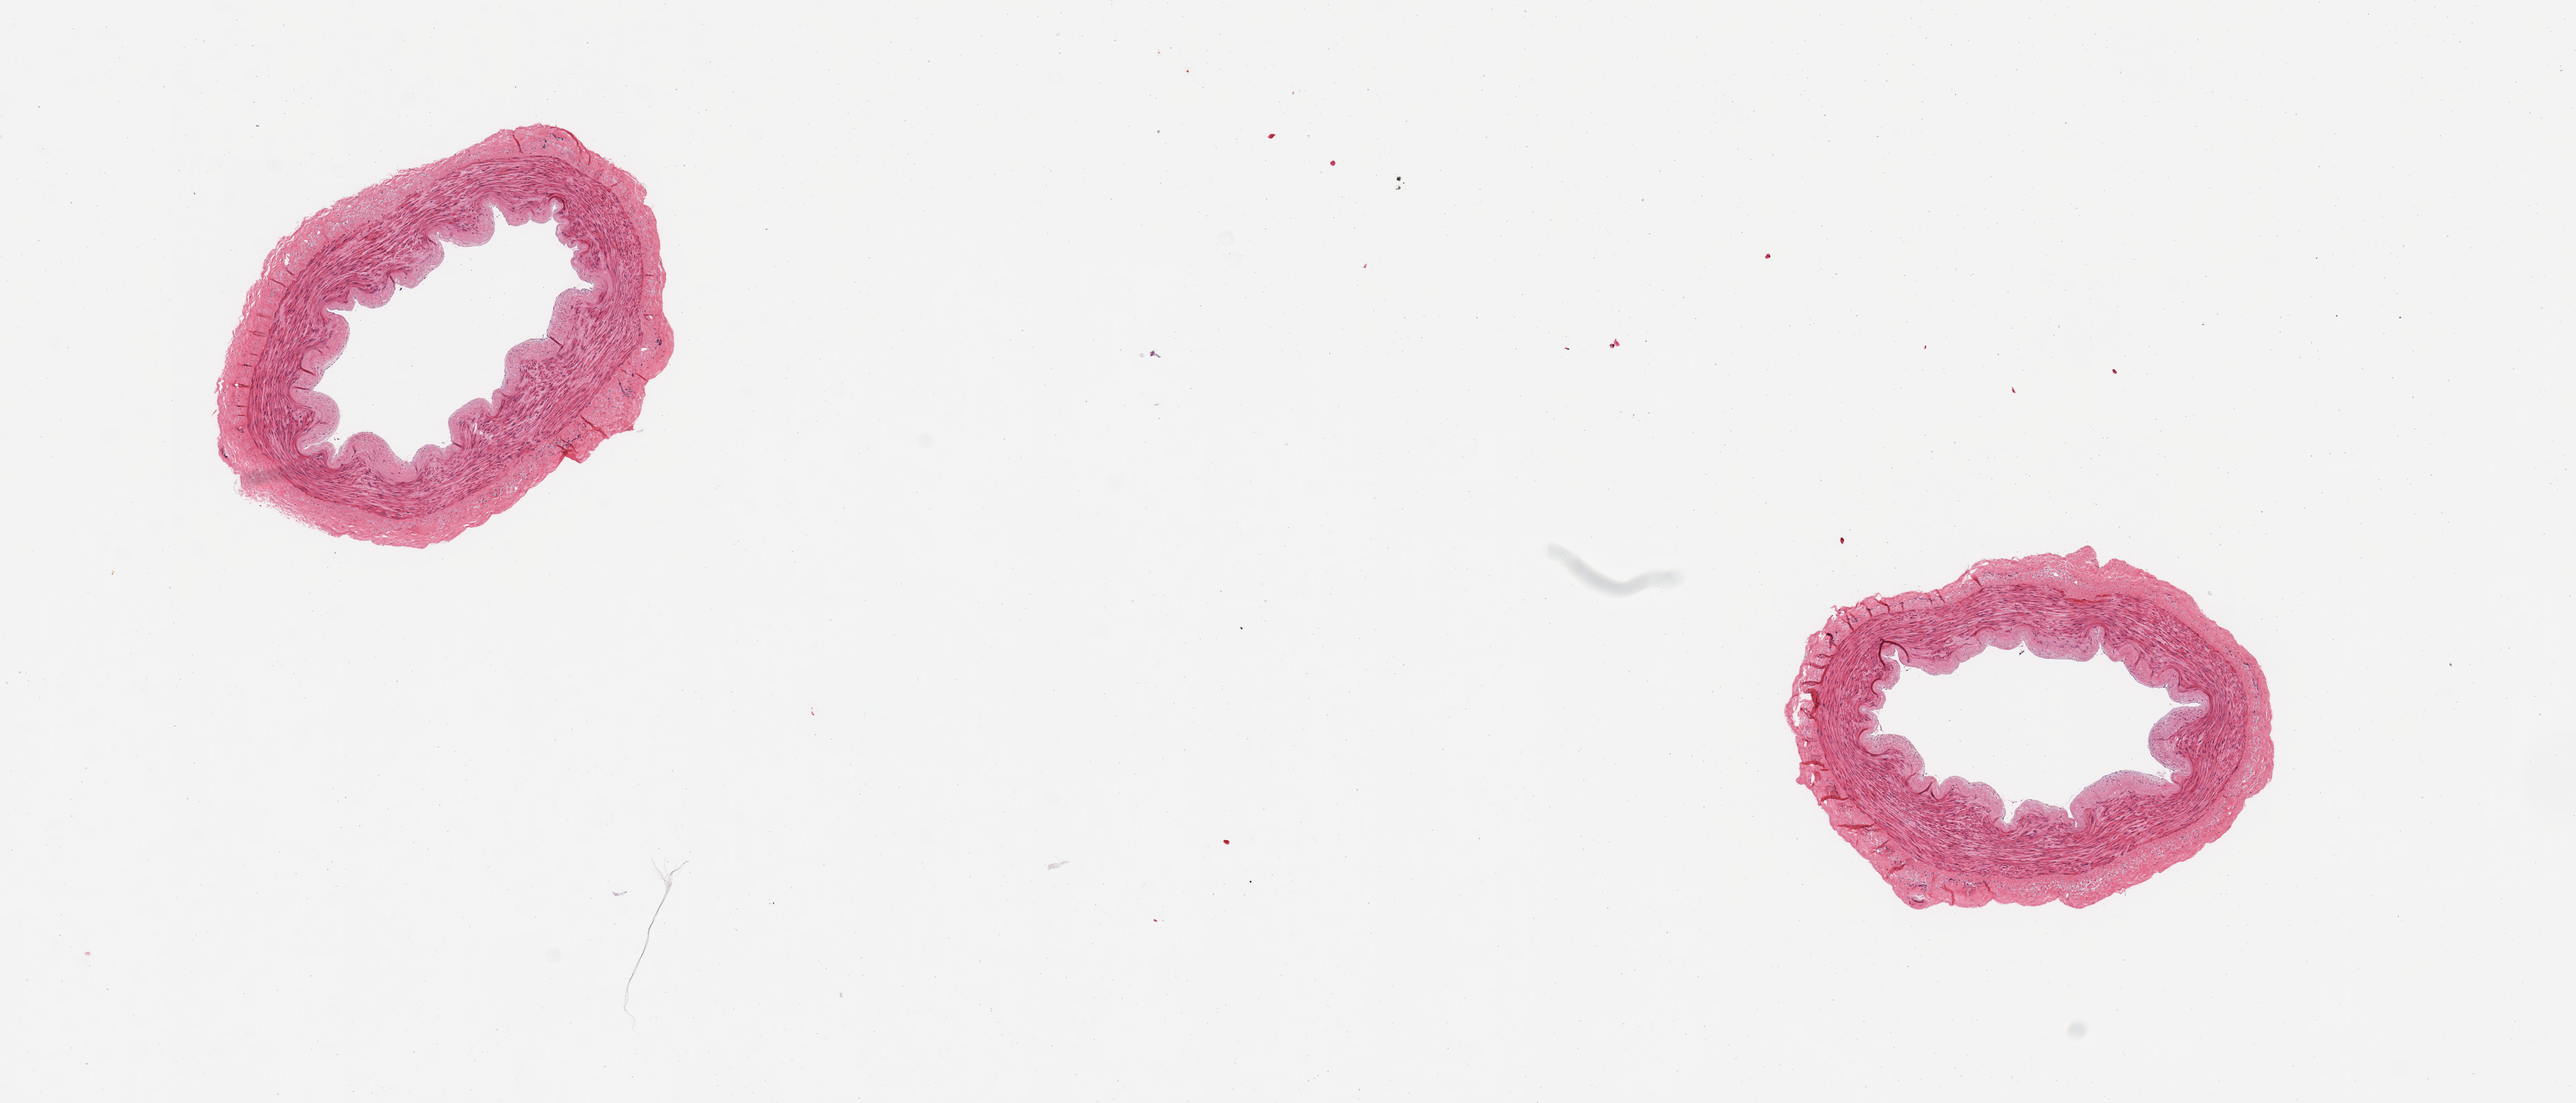
Digitized haematoxylin and eosin-stained section, brightfield — a low-resolution overview of the entire scanned area, about 14.8 x 6.3 mm (from a 20x scan); PAXgene-fixed paraffin-embedded (PFPE) section; target tissue: tibial artery; tissue donor sample. Male donor.
- reviewer comment on this tissue sample: 2 pieces, no atherosis or adherent fat